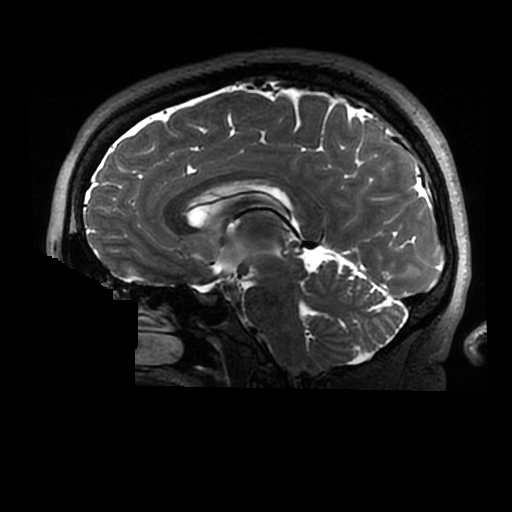
Brain MRI from a brain-tumour surgery series, one sagittal slice. Slice 149 of 320 in the series (ordered by position). 512 × 512 image matrix, field of view 240 × 240 mm. From the clinical record (not read from this slice): histopathology: Astrocytoma; WHO grade: 2; IDH mutation: yes.
Outlined on this slice (expert manual segmentation):
- tumour: bounding box (x1, y1, x2, y2) in pixels: (279, 208, 290, 241)